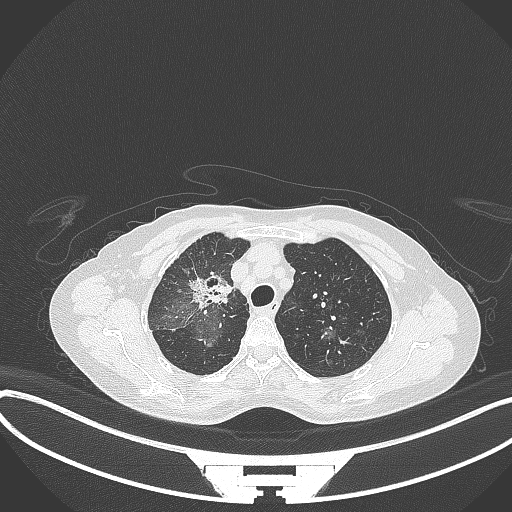
Chest CT, one axial slice. Slice 246 of 284 in the series (ordered by position). 120 kVp. Lung window (W 1500 / L -600 HU). 1 mm slice thickness. 512 × 512 image matrix, field of view 400 × 400 mm. Female patient, age 59 years. From the clinical record (not read from this slice): clinical TNM (as recorded): T3 N0 M0; histopathological grade: G1.
Outlined on this slice (bounding box drawn by a radiologist):
- lung tumour (recorded histology: adenocarcinoma): box from (x=188, y=269) to (x=236, y=311) px